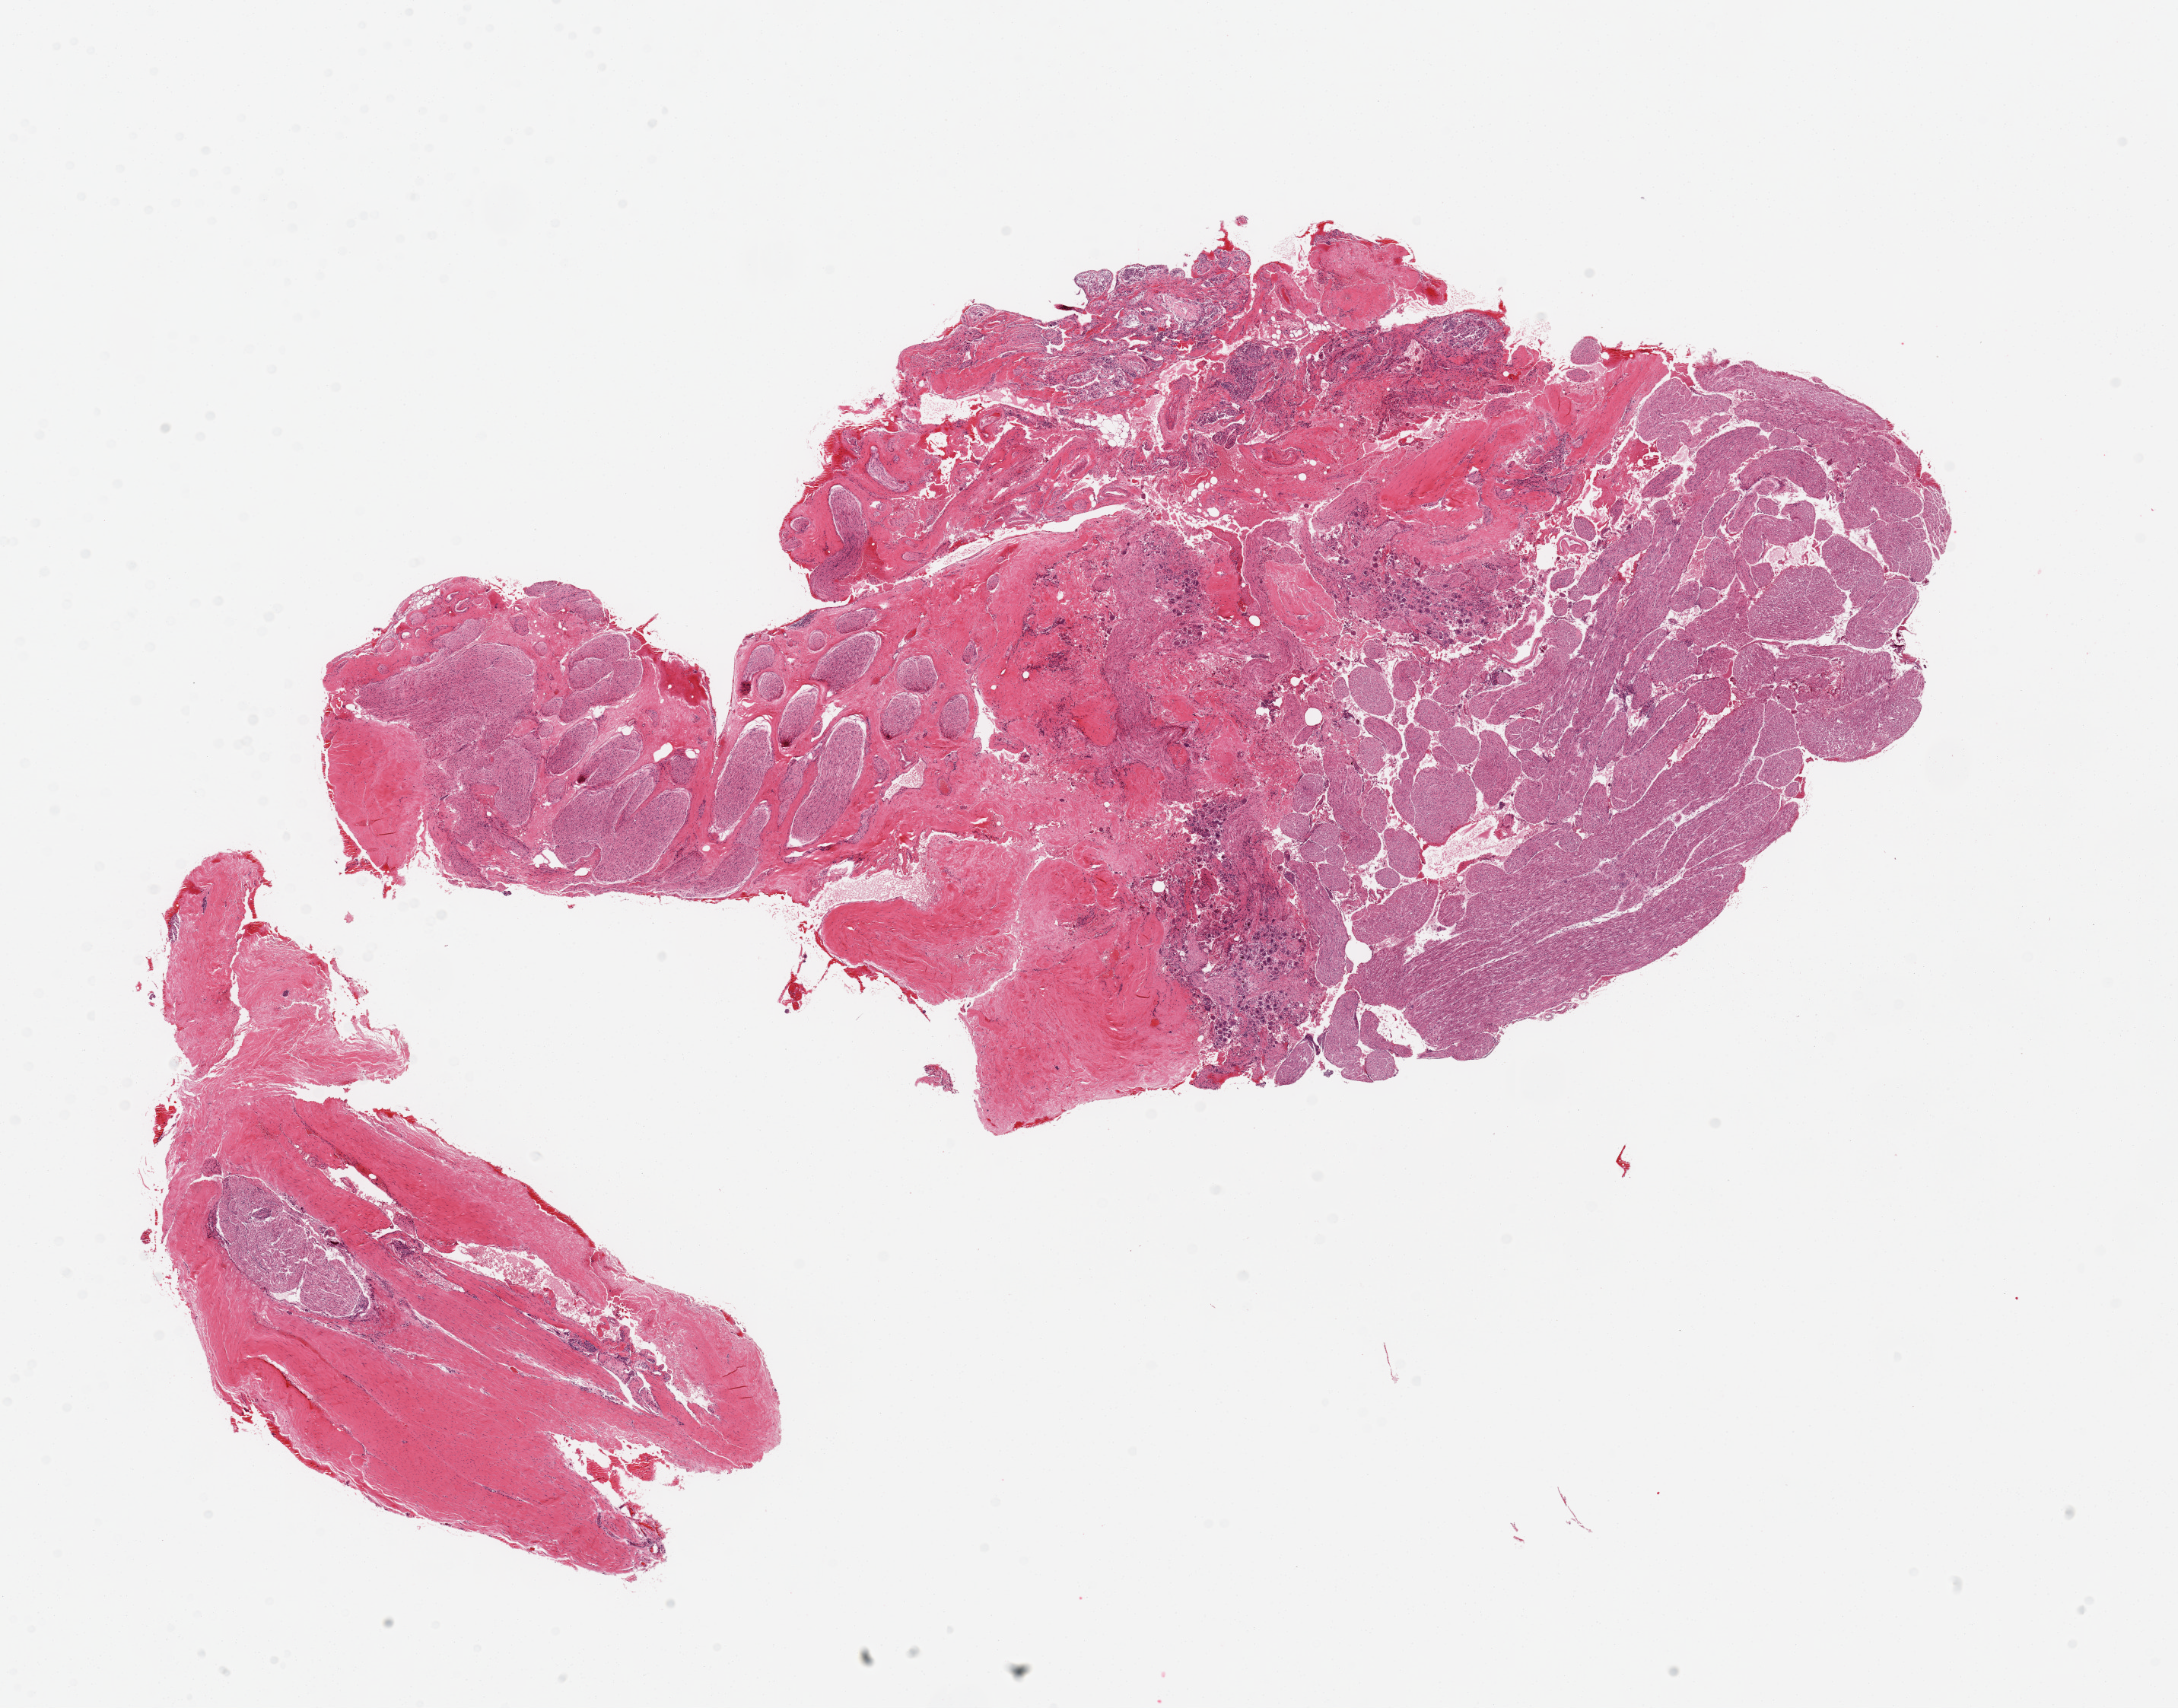
Digitized H&E-stained section — low-resolution overview of the scanned area, about 22.6 x 17.8 mm (from a 20x scan). PAXgene-fixed, paraffin-embedded tissue. Target tissue: pituitary. Donor tissue sample. Donor: male.
Reviewer comment on this tissue sample: 1 piece; no pituitary, only nerves and stroma.